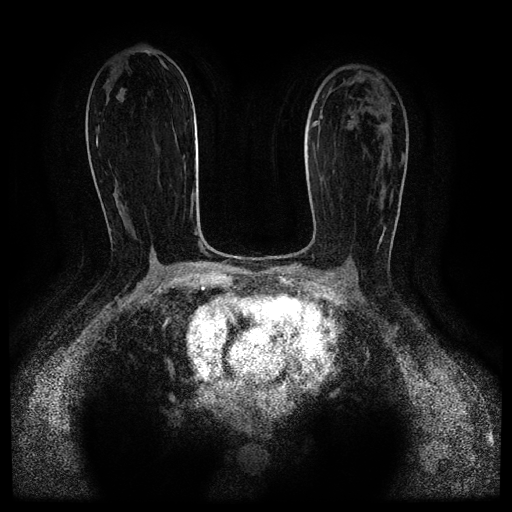
Breast MRI (dynamic contrast-enhanced, multi-phase), one axial slice; dynamic contrast-enhanced series, time point 2 of 5 at this slice position (early post-contrast); 1.5 T; TE 2.6 ms, TR 5.3 ms; 512 × 512 image matrix, field of view 350 × 350 mm. Patient: female, 52 years.
Annotated regions visible in this slice (semi-automatically segmented with operator editing):
- breast lesion (labelled 'tumour' in the annotation; benign lesions carry a separate 'benign' label): bounding box [x1, y1, x2, y2] px = [381, 124, 387, 130]